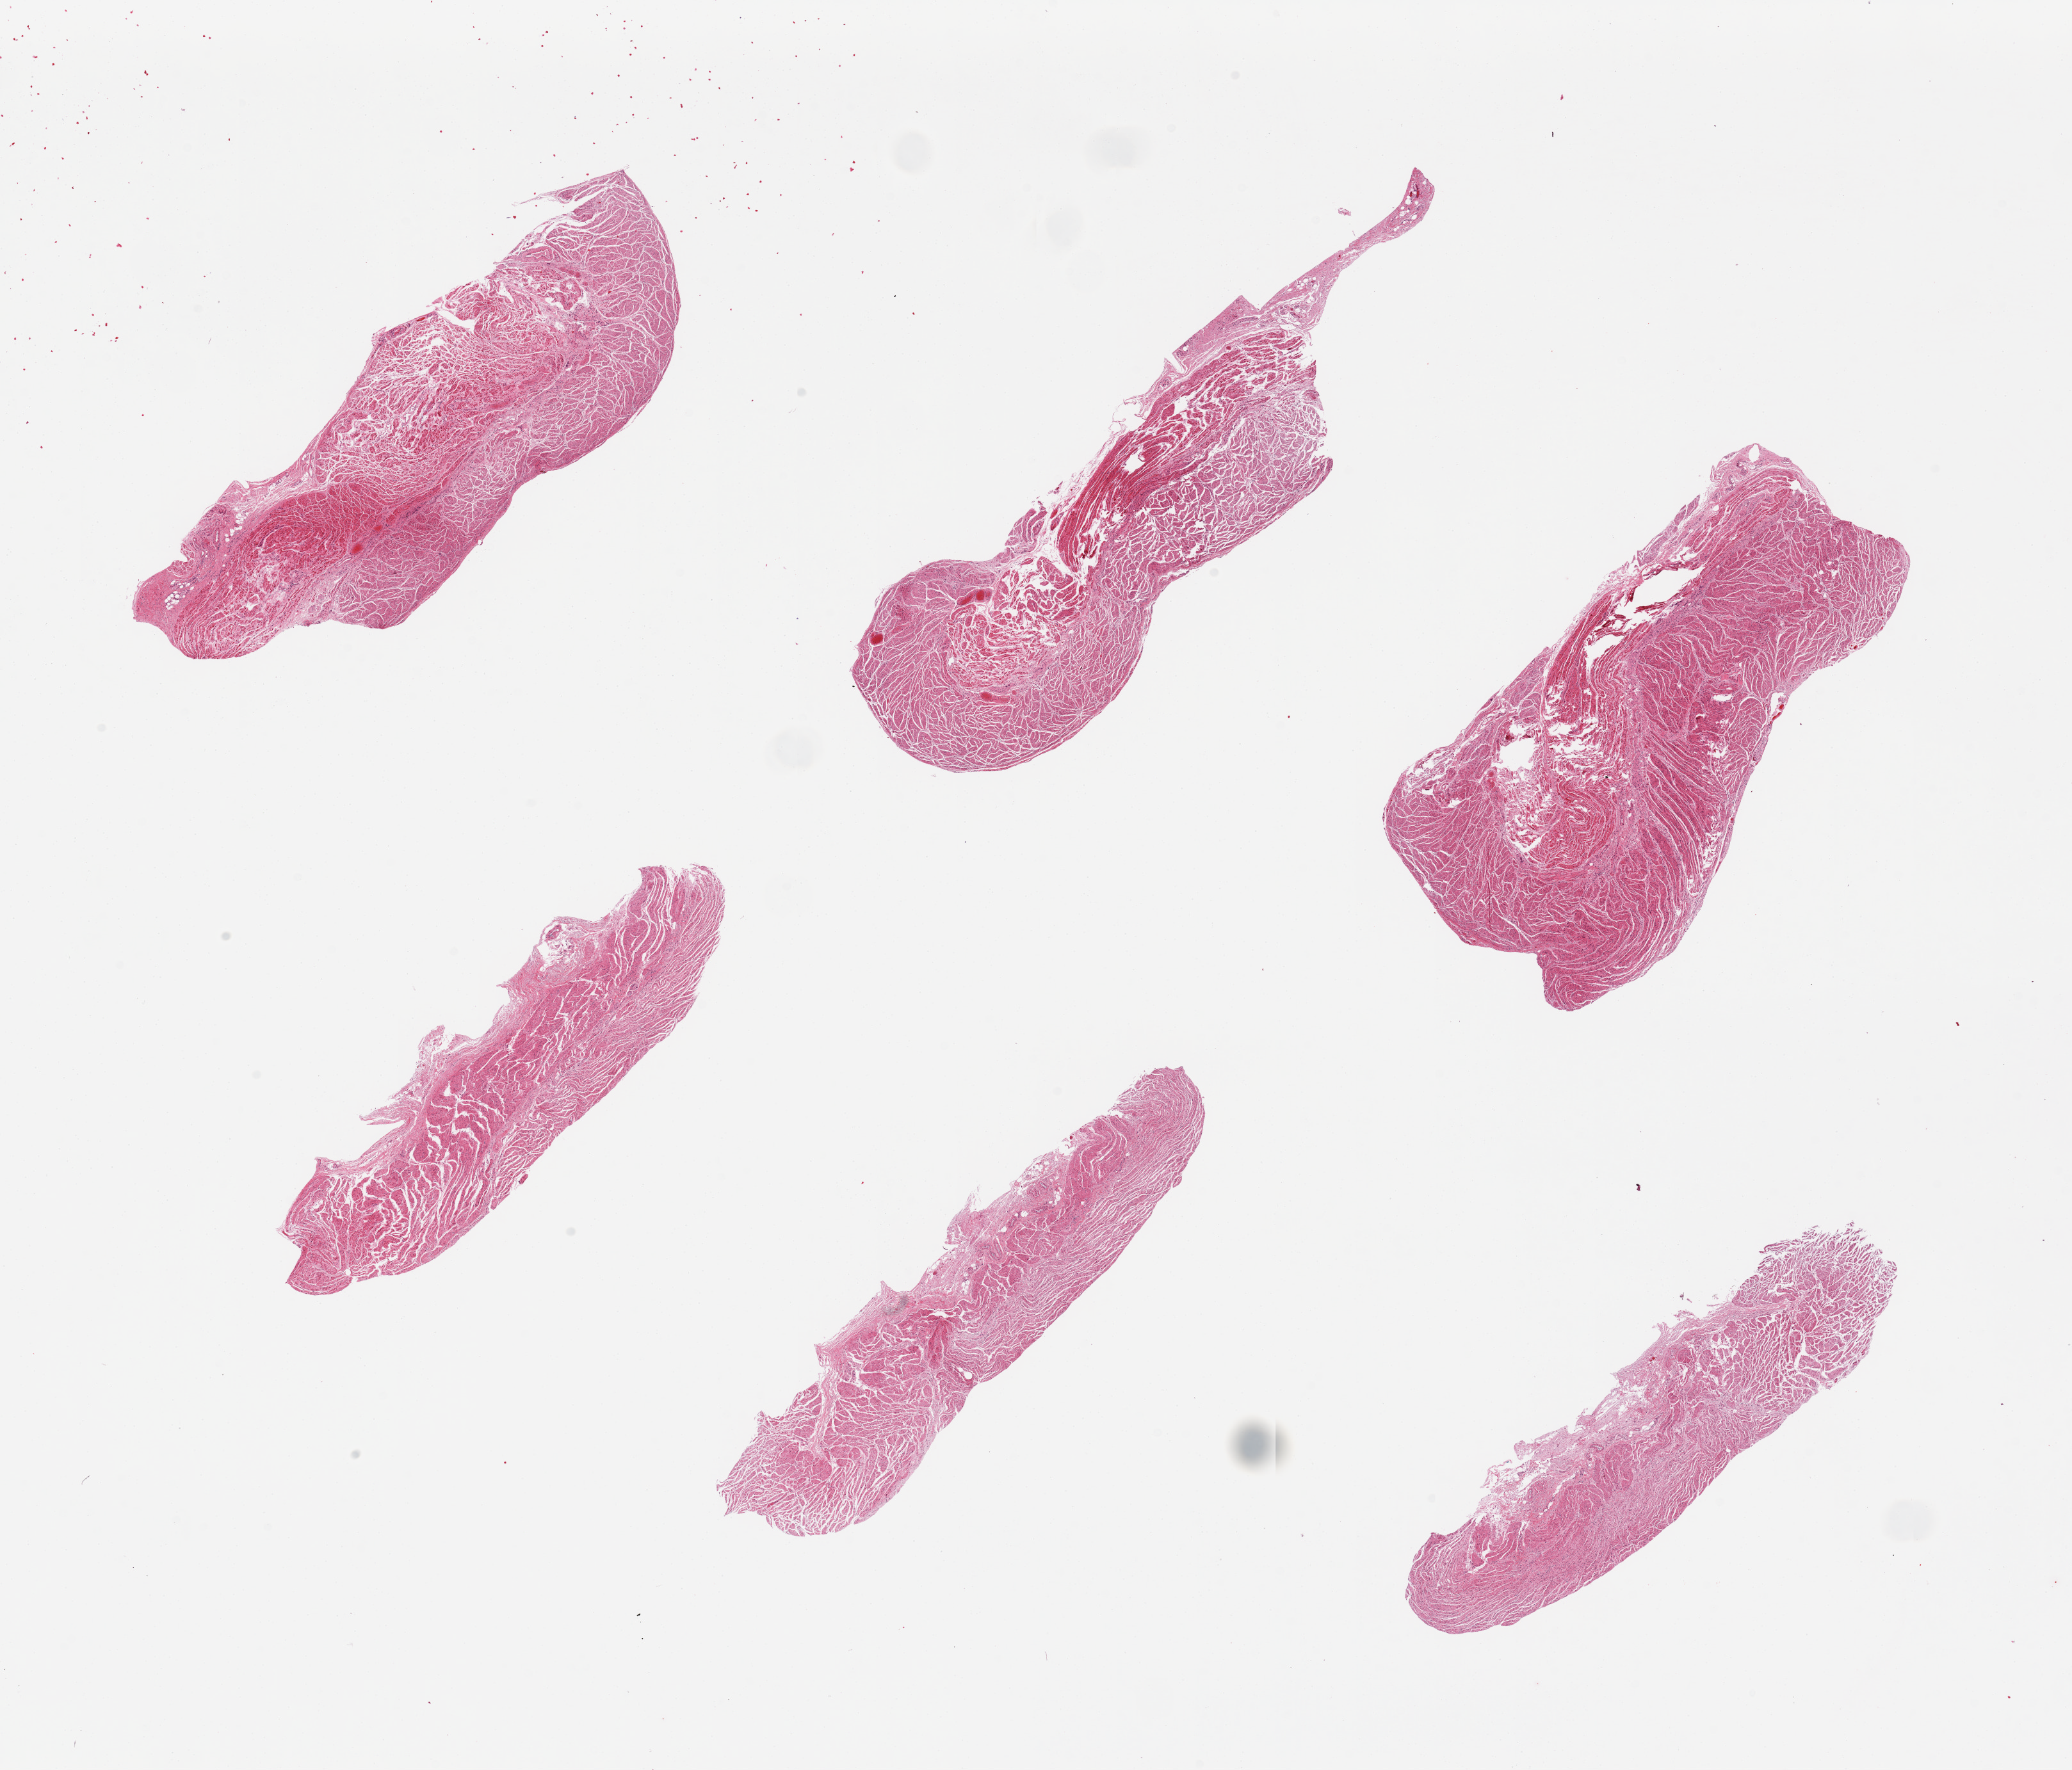
Whole-slide image, H&E stain, shown as a low-resolution overview of the whole scanned area (about 25.6 x 21.9 mm); PAXgene-fixed, paraffin-embedded tissue; target tissue: gastroesophageal junction; donor tissue sample. Donor: female.
Pathologist's review note for this sample: 6 pieces; well dissected muscle.